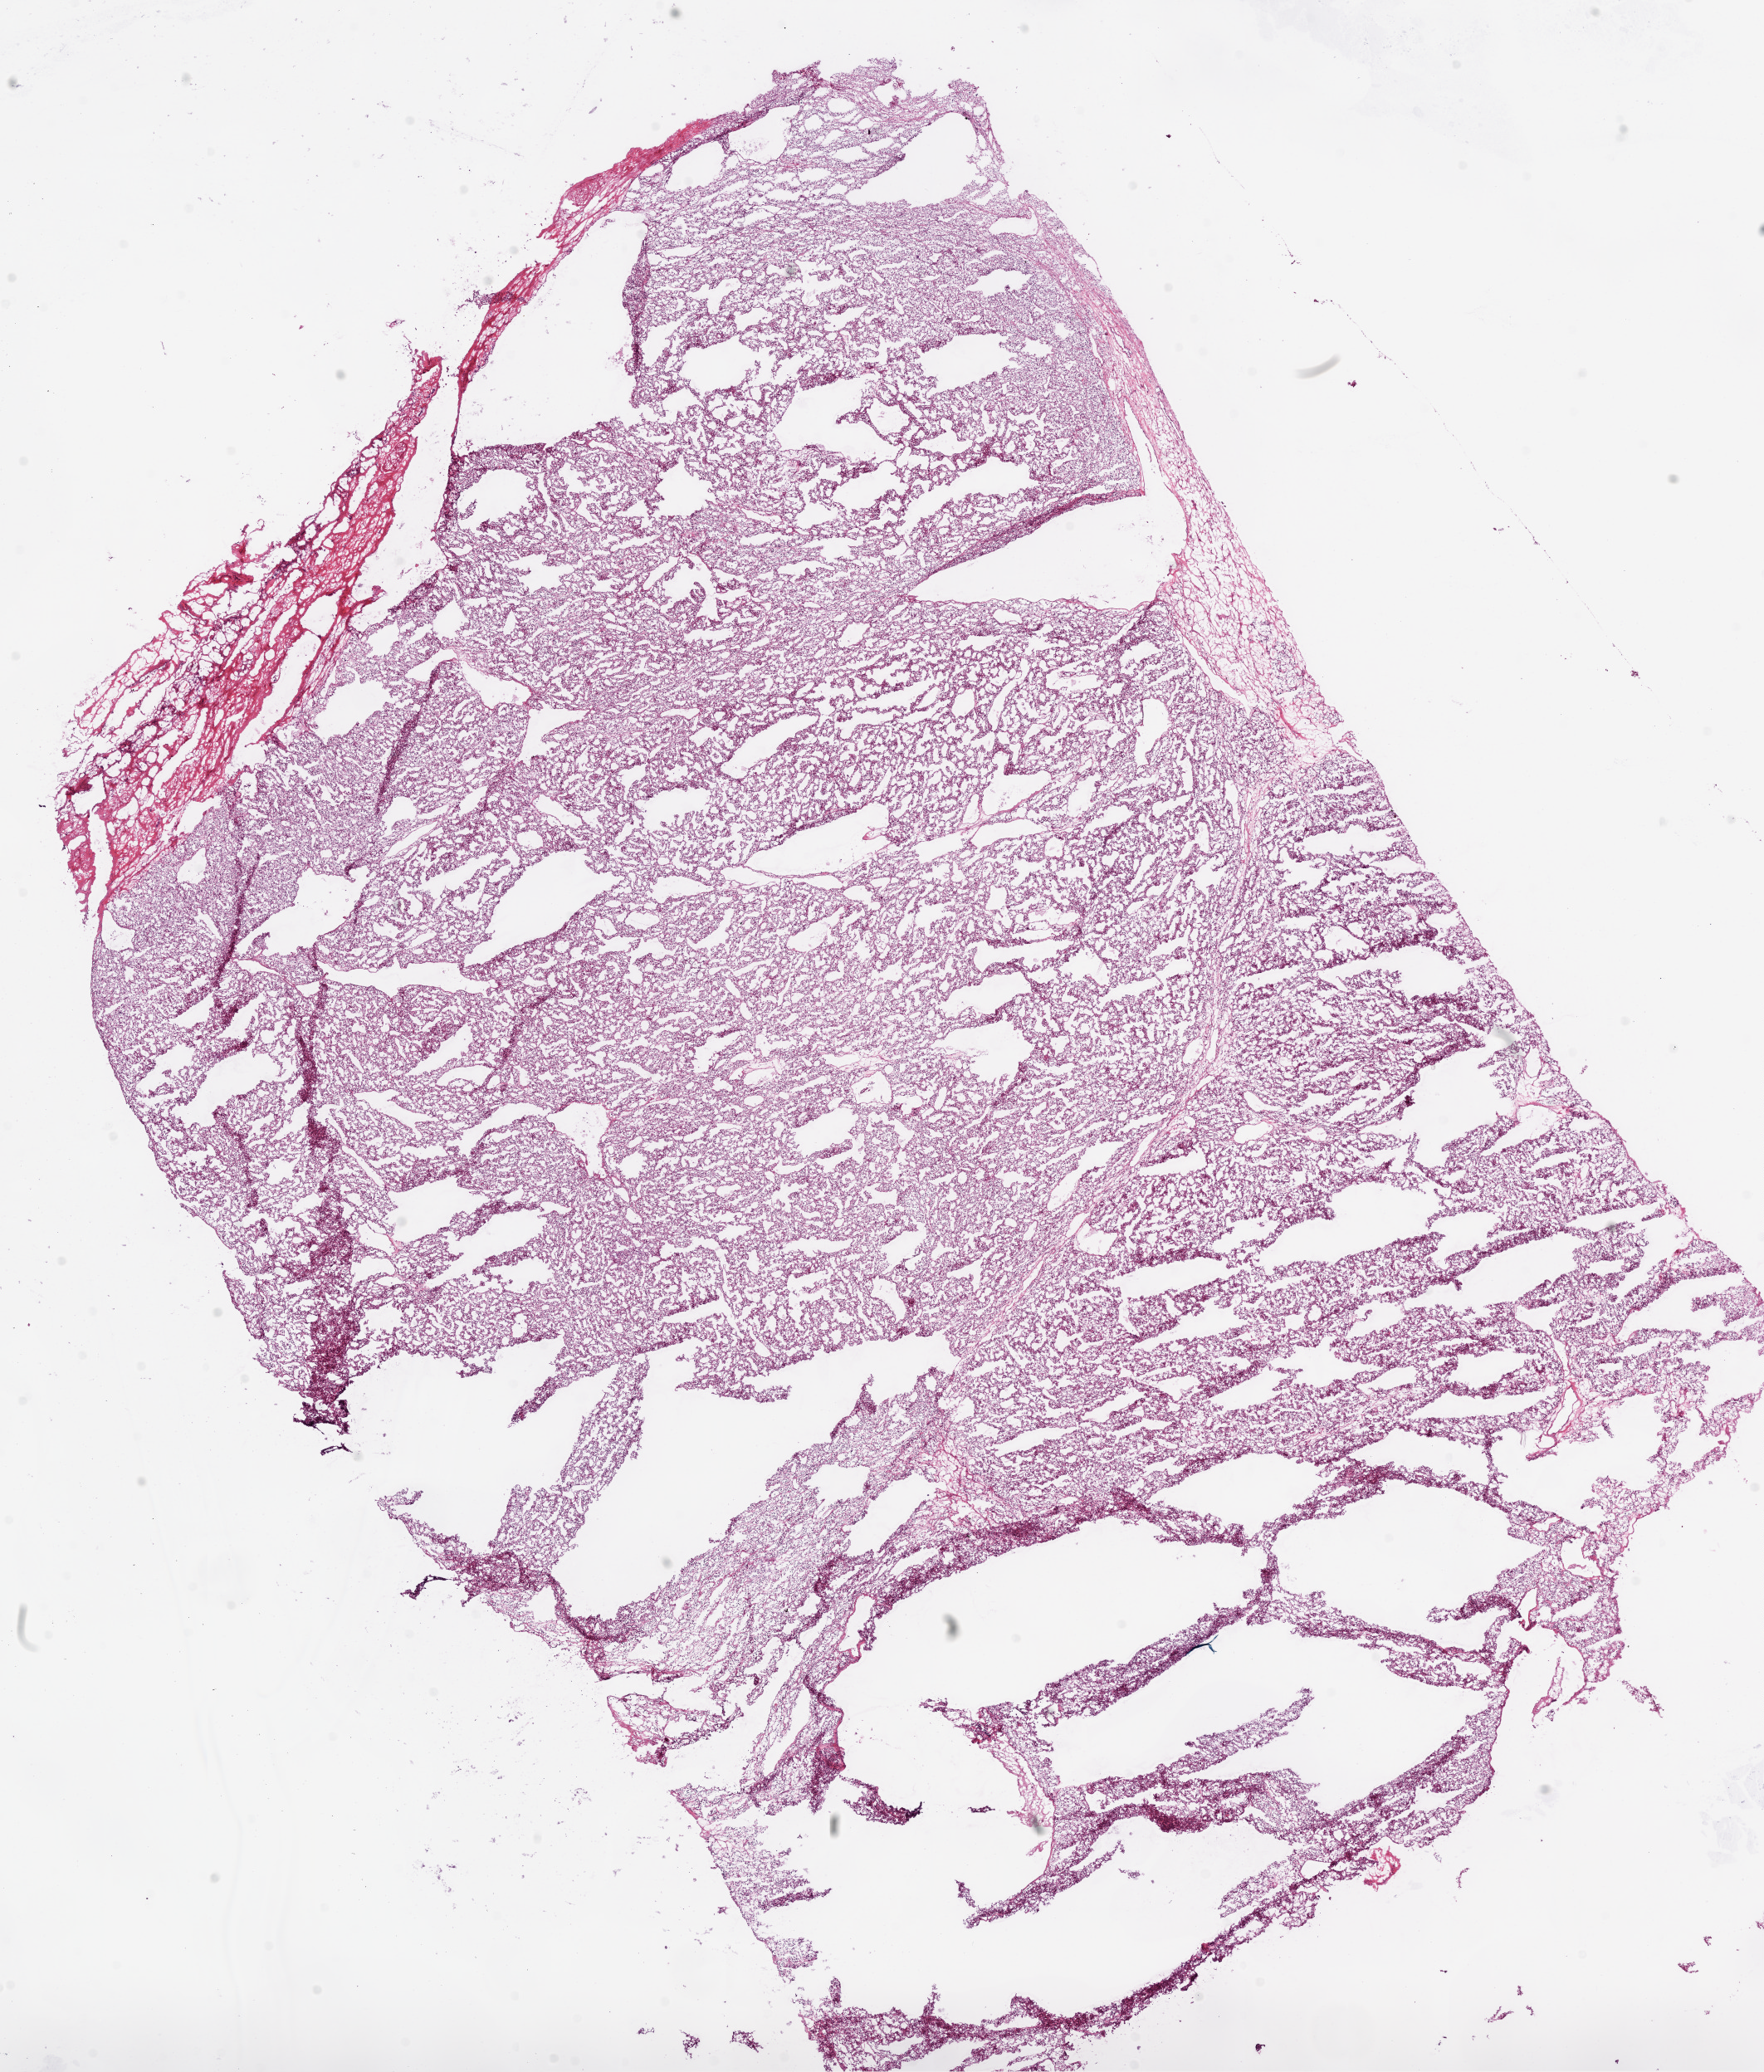
Digitized H&E tissue section (whole slide), low-resolution overview of the scanned area, about 17.1 x 20.0 mm; frozen section; kidney, primary tumour sample. Female, age 51 years at initial diagnosis. Histologic grade: G2 (moderately differentiated). Slide review estimates, as recorded: tumour cells 95%, tumour nuclei 90%, normal cells 0%, stromal cells 5%, necrosis 0%.
Laterality: left. Diagnosis: Clear cell adenocarcinoma, NOS. AJCC pathologic stage: III.